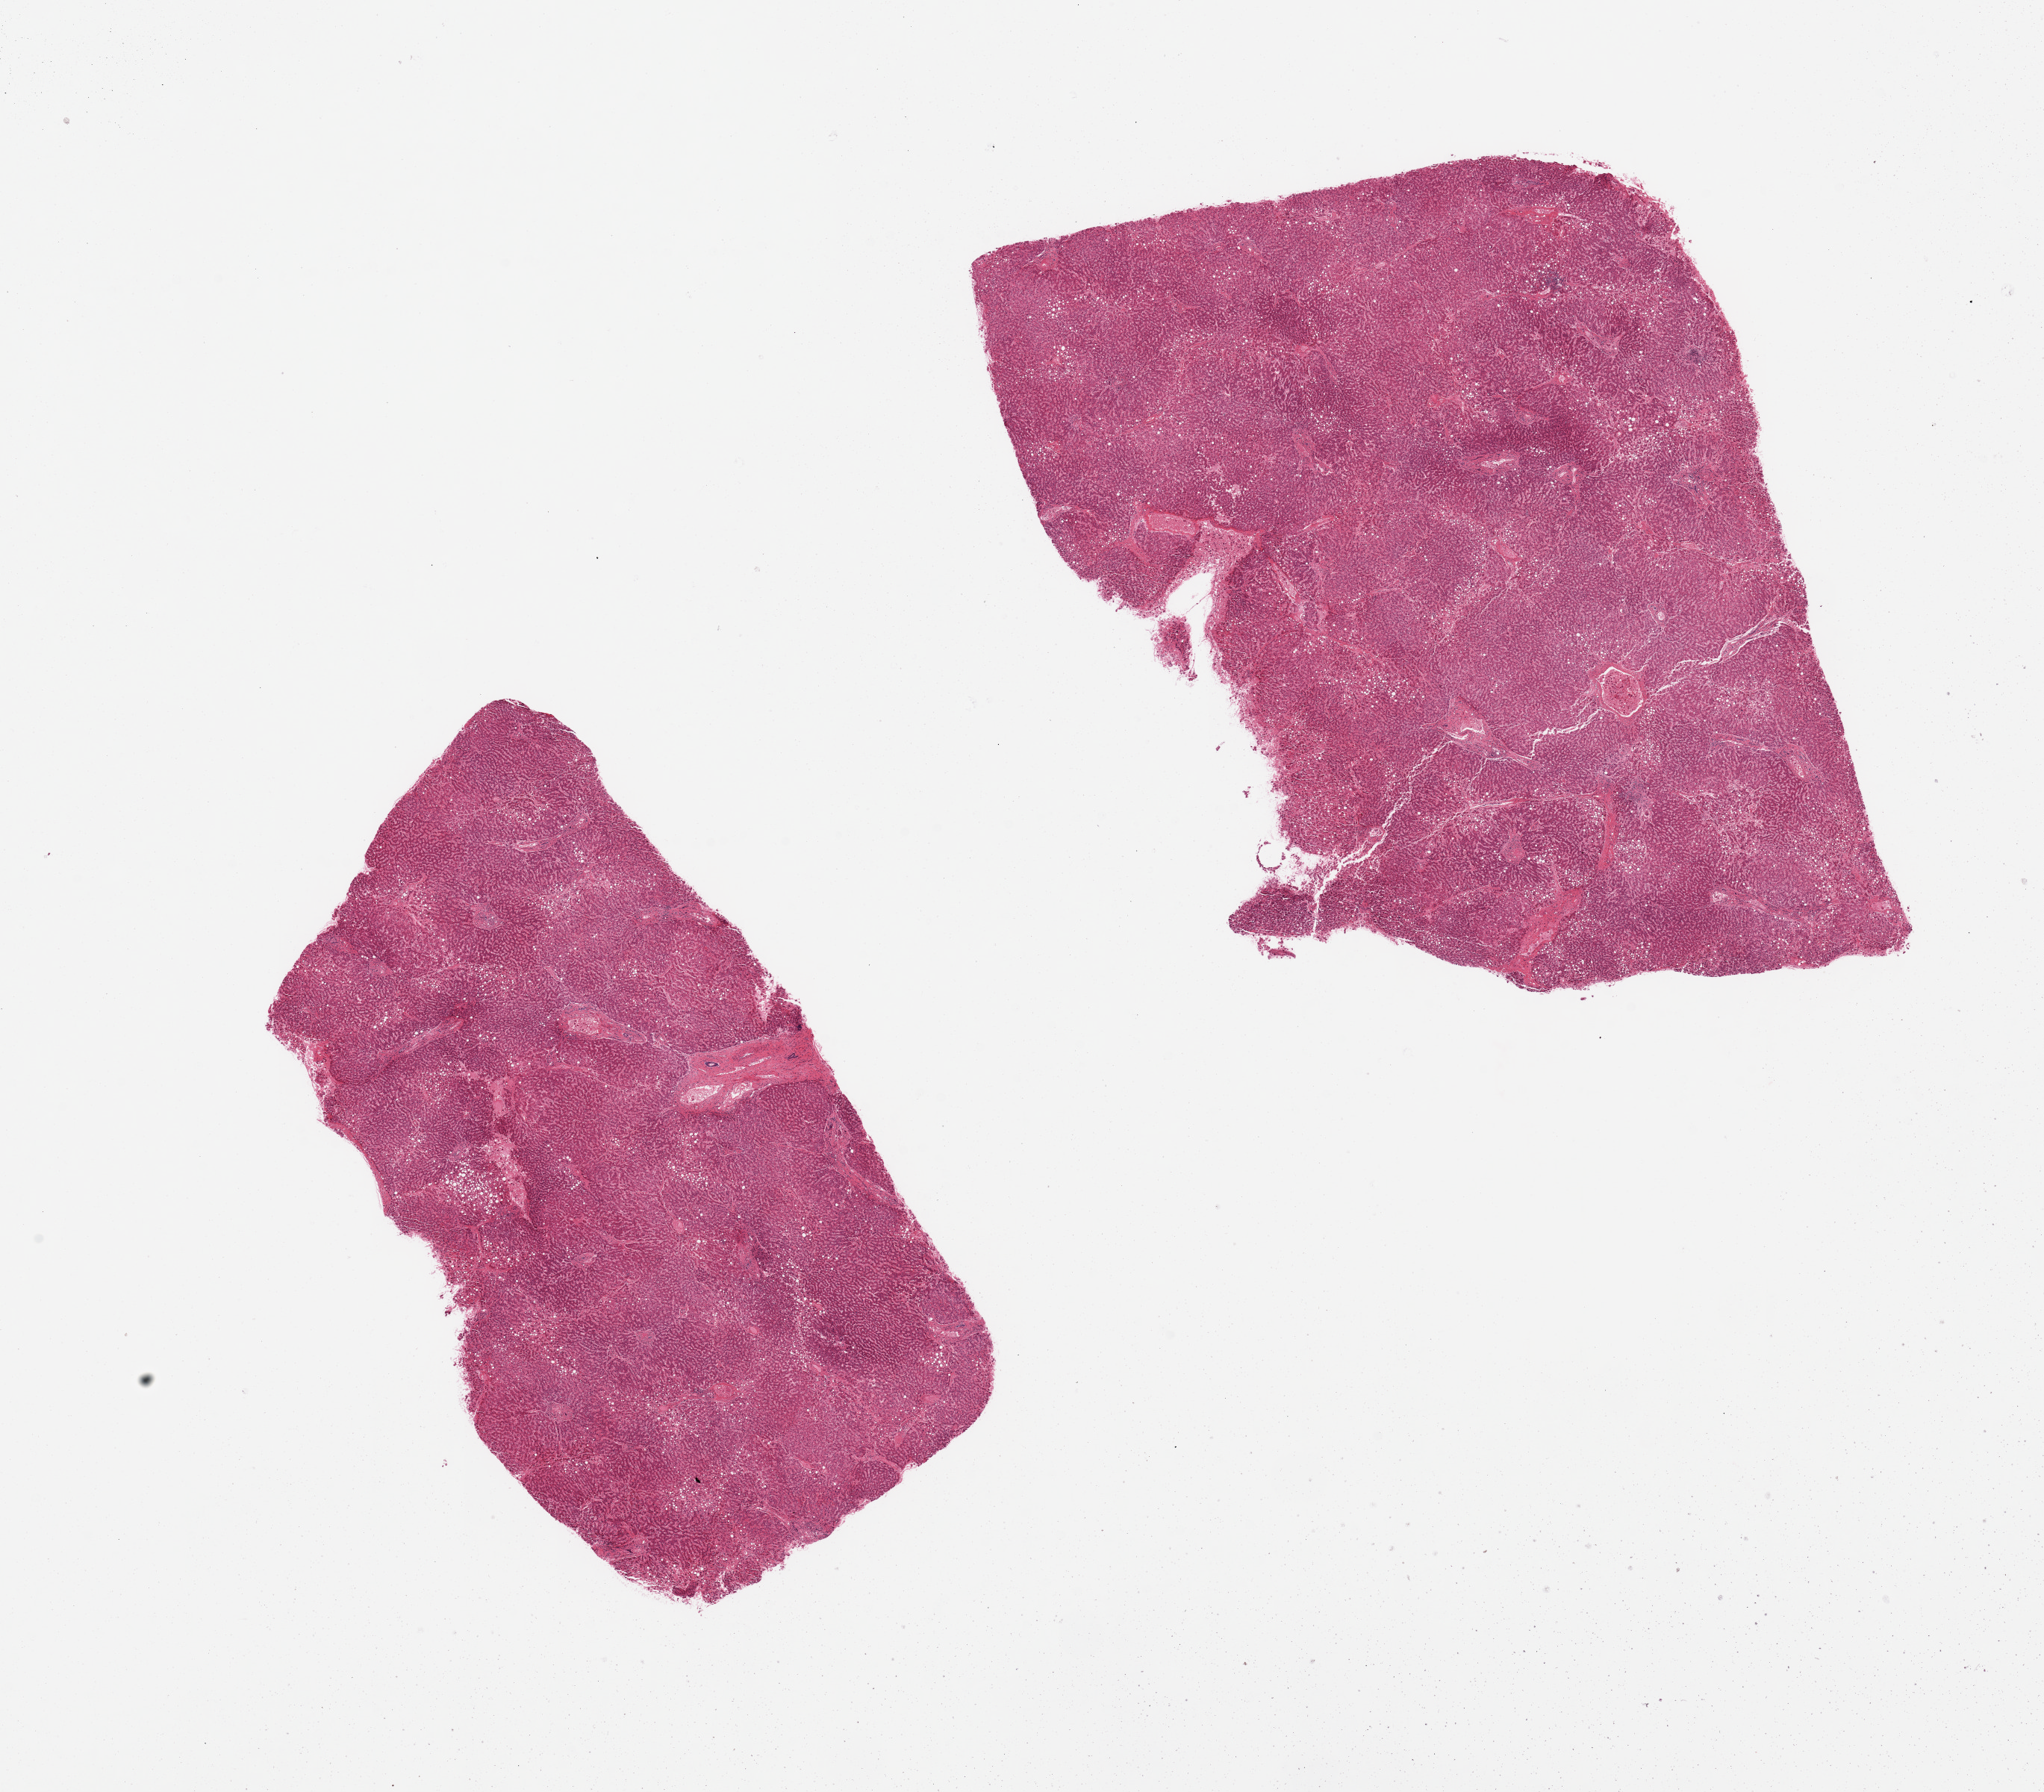
H&E whole-slide image, brightfield — whole scanned area (about 21.7 x 19.0 mm, slide scanned at 20x) shown as a low-resolution overview. PAXgene-fixed, paraffin-embedded tissue. Target tissue: liver. Donor tissue sample.
Reviewer comment on this tissue sample: 2 pieces, mild macrovesicular steatosis (~10-20%).